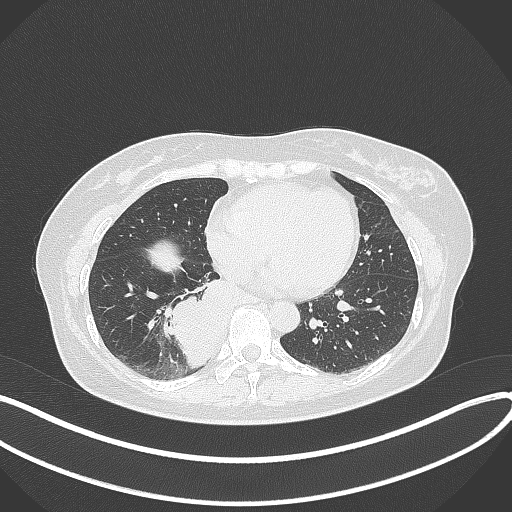
Chest CT, one axial slice; position 128 of 331 along the scan axis; lung window (W 1500 / L -600 HU); 512 × 512 image matrix, field of view 400 × 400 mm. Female patient, age 54 years. Case-level facts recorded for this patient, not image findings: clinical TNM (as recorded): T4 N0 M0.
Outlined on this slice (rectangle marked by the reading radiologist):
- lung tumour (recorded histology: adenocarcinoma): bounding box (x1, y1, x2, y2) in pixels: (162, 271, 241, 379)